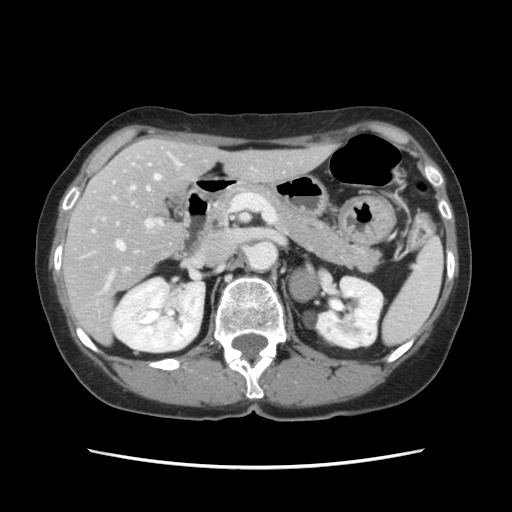
Contrast-enhanced abdominal CT, one axial slice; slice 67 of 120 in the series (ordered by position); intravenous contrast given; soft-tissue window (W 400 / L 40 HU); 2.5 mm slice thickness; 512 × 512 image matrix, field of view 330 × 330 mm. Female patient, age 70 years. From the clinical record (not read from this slice): diagnosis: colorectal cancer liver metastases, imaged before liver resection; multiple liver metastases: no; largest metastasis: 2.5 cm; disease in both lobes: no.
Annotated regions visible in this slice (expert manual segmentation):
- hepatic veins: bounding box (x1, y1, x2, y2) in pixels: (93, 164, 160, 250)
- liver: (64, 139, 328, 342)
- planned liver remnant (the part of the liver to remain after resection): (83, 140, 330, 279)
- portal vein (with intrahepatic branches): (102, 153, 181, 270)